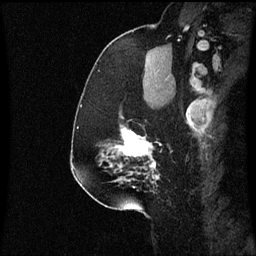
Breast MRI (dynamic contrast-enhanced), one sagittal slice. Position 41 of 60 along the scan axis. Dynamic contrast-enhanced series, image 2 of 3 at this slice position (ordered by acquisition). 1.5 T. TE 4.2 ms, TR 8.9 ms. 2 mm slice thickness. 256 × 256 image matrix, field of view 200 × 200 mm. Female patient, age 58 years. Case-level facts recorded for this patient, not image findings: setting: breast cancer imaged before/during neoadjuvant chemotherapy; receptor status: triple-negative.
Outlined on this slice (semi-automatically segmented with operator editing):
- analysis volume of interest (the breast-tissue region the enhancement analysis was run in; not a lesion): bounding box [x1, y1, x2, y2] px = [104, 126, 161, 179]
- tumour enhancement mask (voxels above the 70 % enhancement threshold inside the analysis volume of interest): [116, 128, 159, 179]